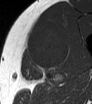
MRI of an extremity soft-tissue mass, one axial slice. Position 37 of 62 along the scan axis. MR volume resampled by the dataset authors to the PET/CT grid (not the native acquisition matrix). 92 × 104 image matrix, field of view 90 × 102 mm. Male patient. Case-level facts recorded for this patient, not image findings: histological type: mixoid liposarcoma; grade: low; site of the primary tumour: left thigh.
Structures marked on this image (expert contour drawn on MRI and transferred to this co-registered scan by the dataset authors):
- gross tumour volume (mass): box from (x=26, y=26) to (x=68, y=71) px